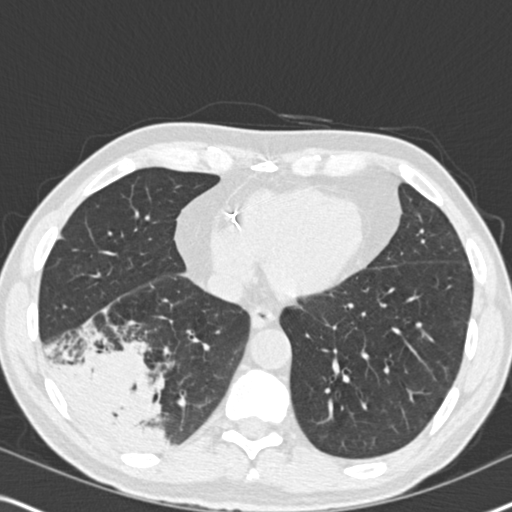
Low-dose screening chest CT, one axial slice; 120 kVp; lung window (W 1500 / L -600 HU); 2 mm slice thickness; 512 × 512 image matrix.
Annotated regions visible in this slice (outlined manually by an expert reader):
- lesion 1 (tumor, lower lobe of right lung): bounding box [x1, y1, x2, y2] px = [55, 349, 169, 449]